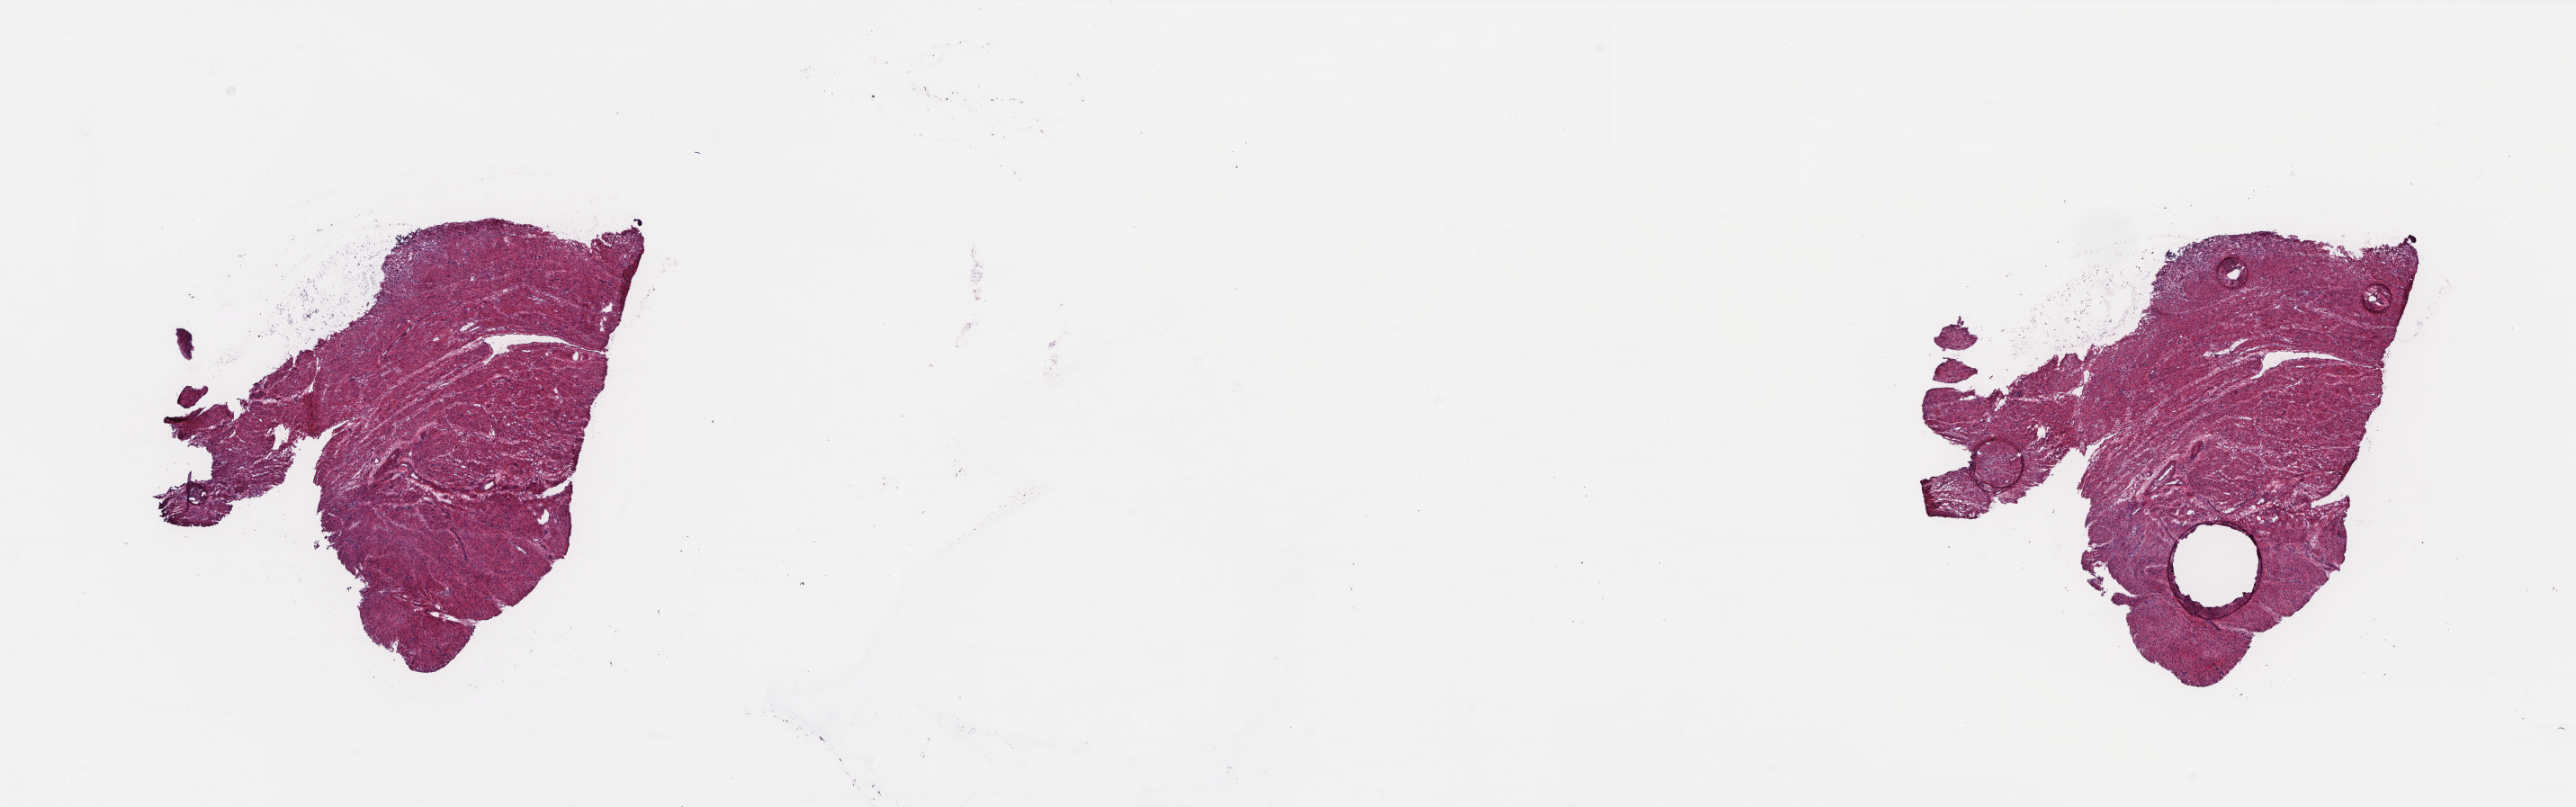
H&E-stained whole-slide image — shown as a low-resolution overview of the whole scanned area (about 23.1 x 7.2 mm), frozen section from the top of the tissue portion, sample: solid tissue normal (non-tumour tissue), uterus. Patient: female, age at initial diagnosis 77 years. Composition of this section per pathologist review: tumour cells 0%, tumour nuclei 0%, normal cells 100%, stromal cells 0%, necrosis 0%. Inflammatory infiltration, as recorded: lymphocyte infiltration 60%, monocyte infiltration 15%, neutrophil infiltration 5%.
This section: solid tissue normal (non-tumour) sample from the same patient. Patient diagnosis: Mullerian mixed tumor.